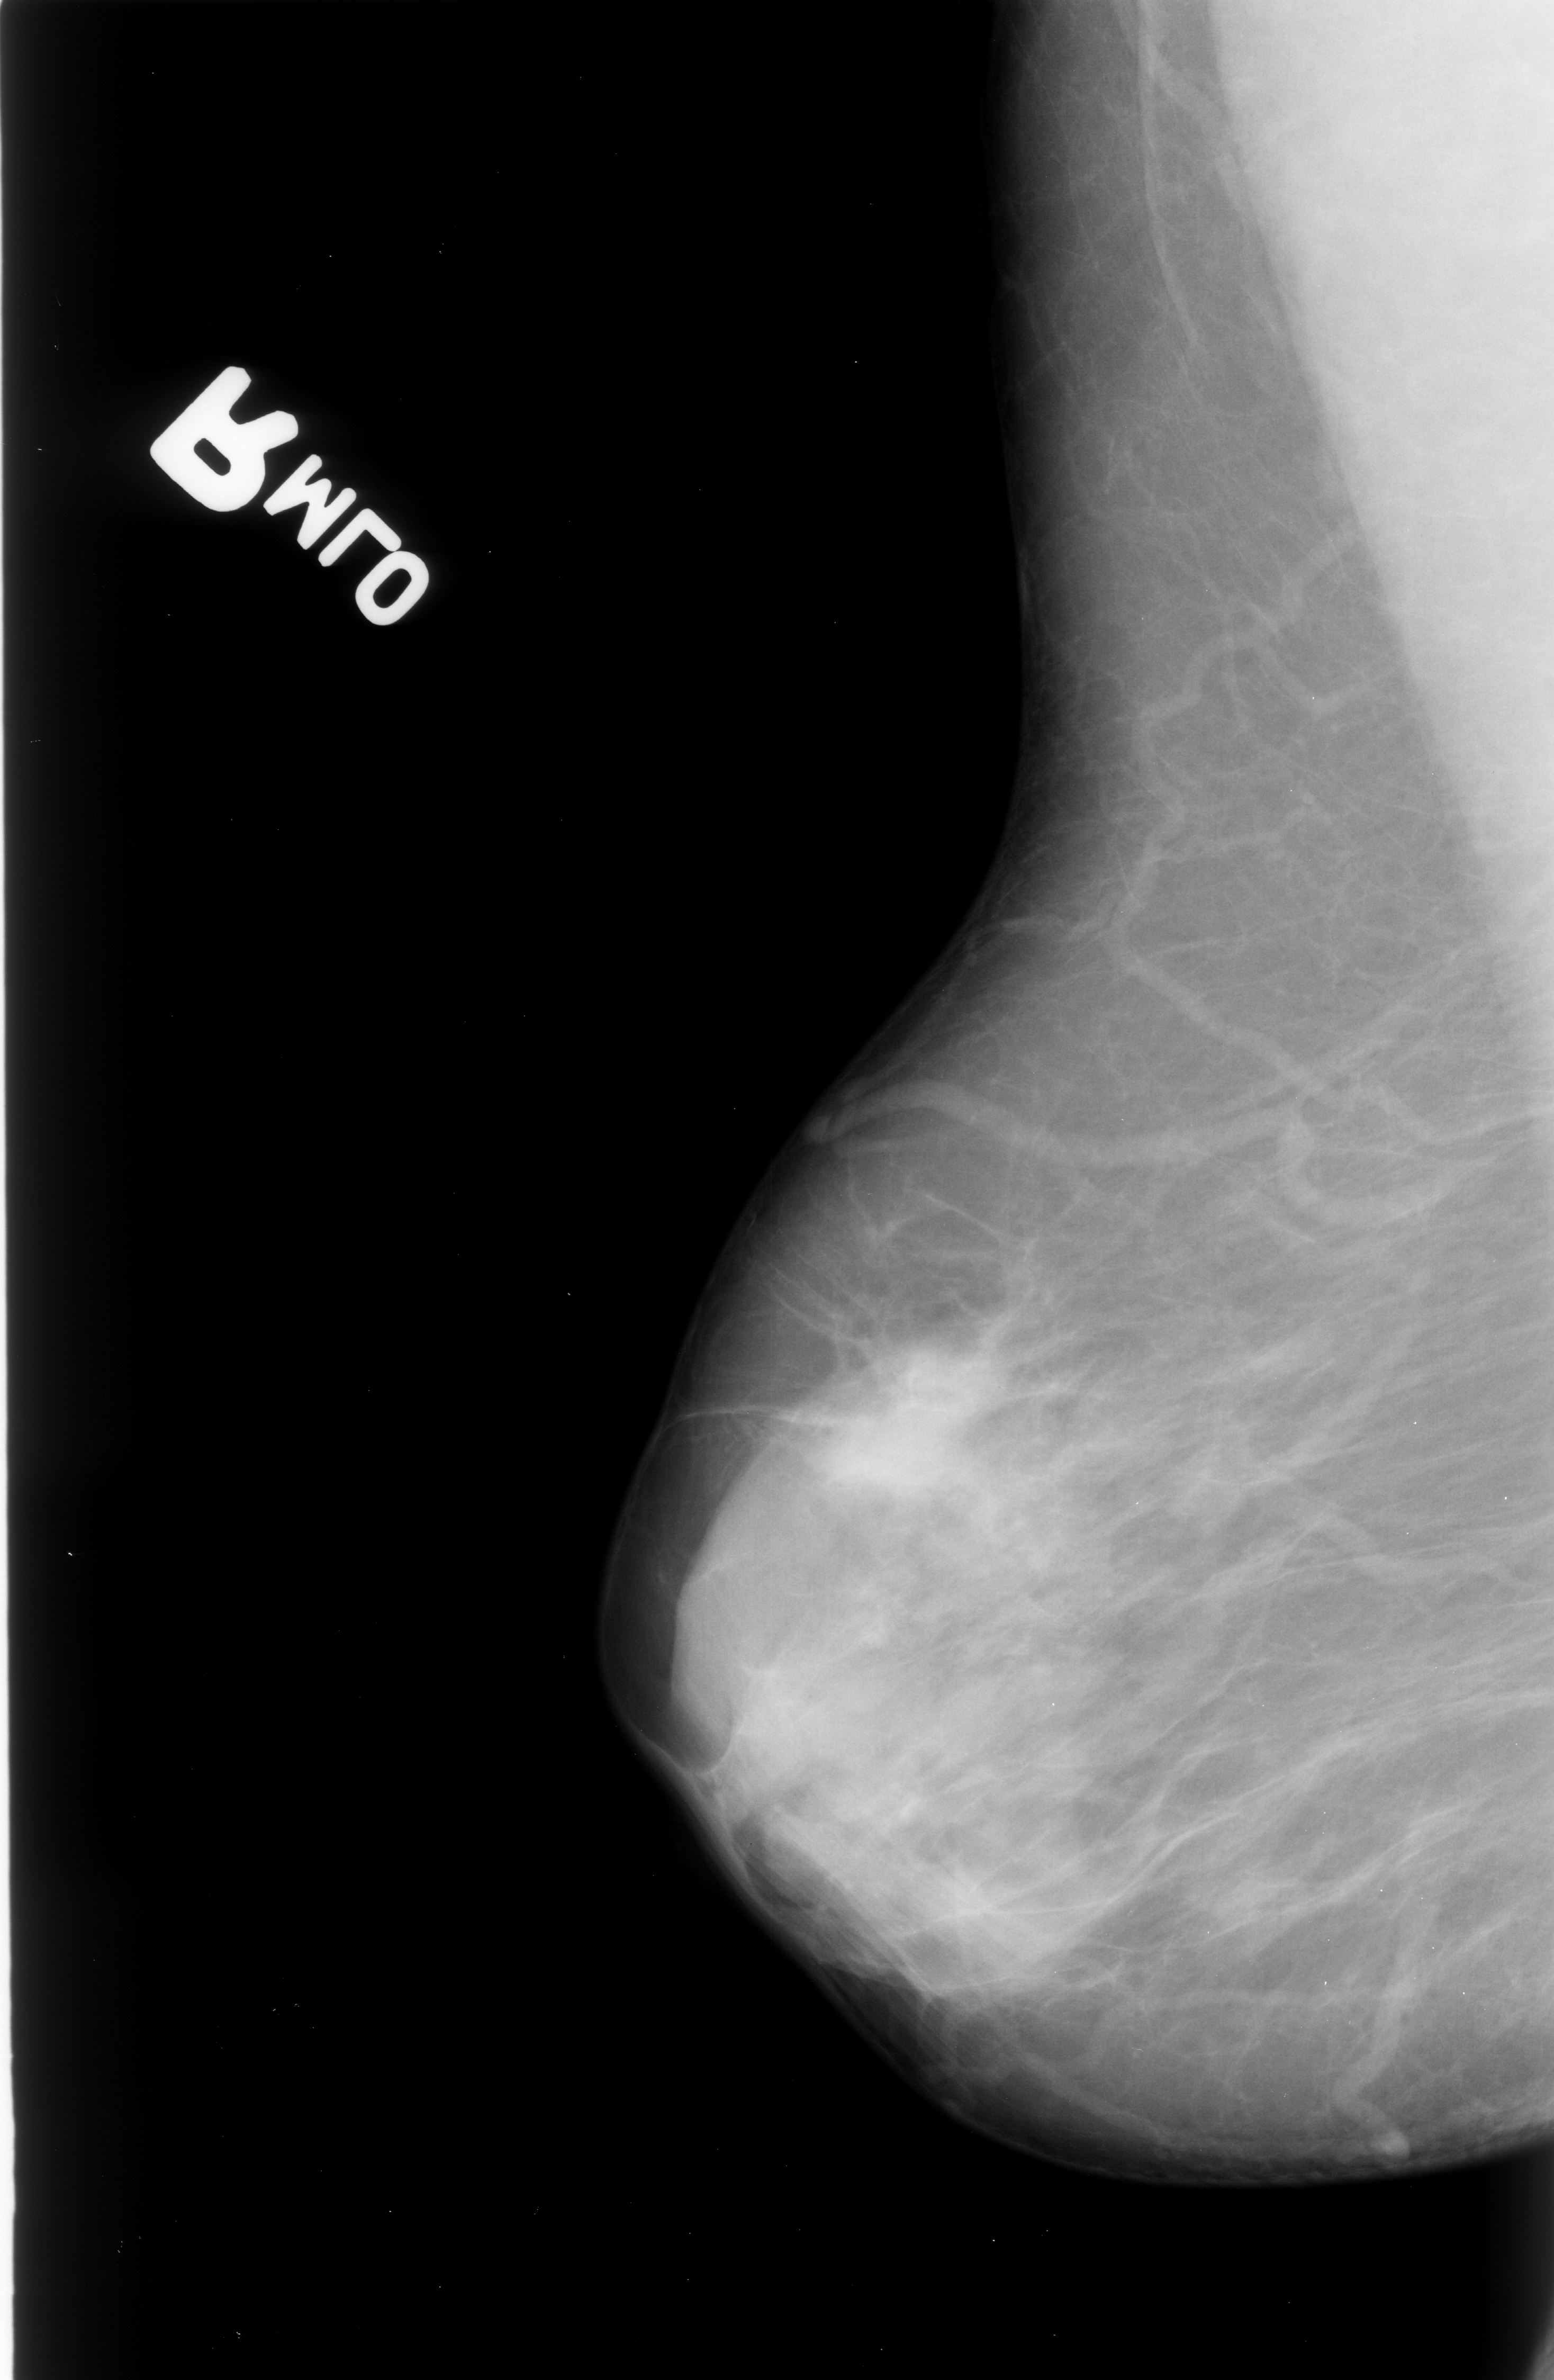
Scanned film-screen mammogram. Right breast. MLO view. 1554 × 2380 image matrix.
Marked abnormalities (boxes around the expert regions of interest):
- mass, shape irregular / architectural distortion, margins obscured / spiculated; BI-RADS assessment category 4; pathology (as recorded): malignant: bounding box <789,1392,968,1522> (left, top, right, bottom; pixels)